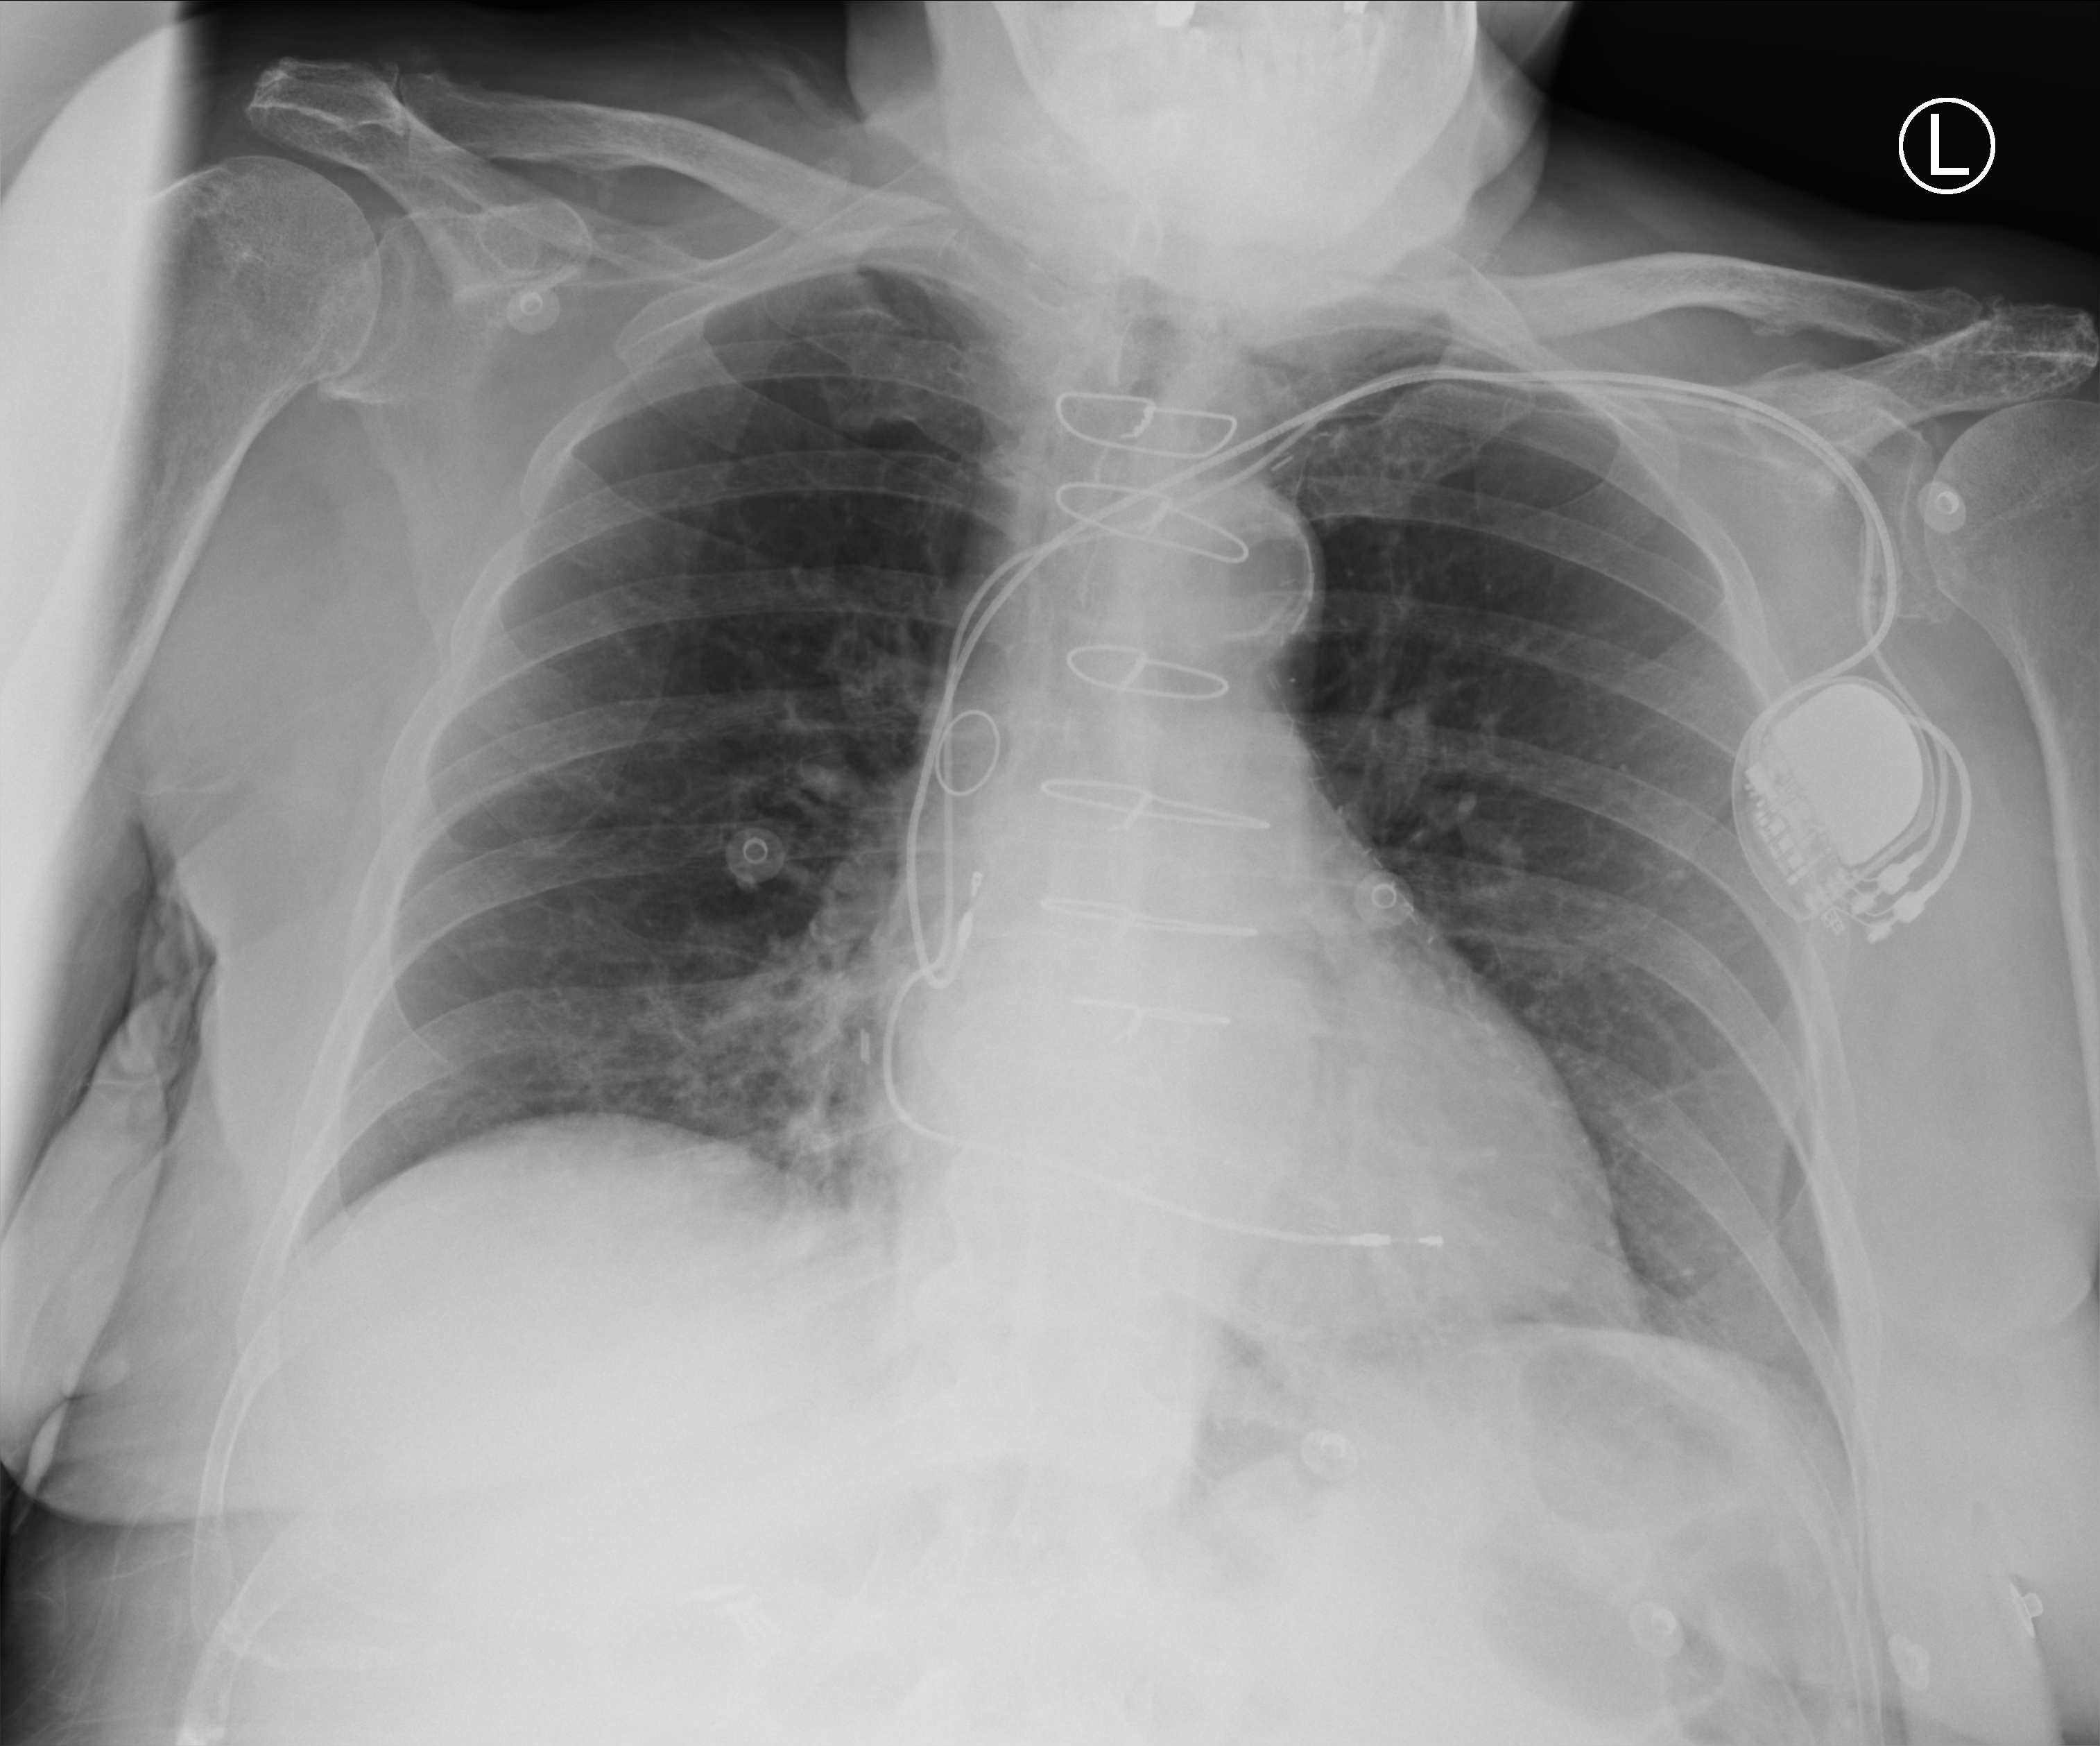
Bedside chest radiograph (computed radiography); anteroposterior (AP) projection. Female patient hospitalised with COVID-19, age 75–90 years.
From the hospital-stay record, not from the radiograph (when in the stay this image was taken is not recorded):
- admitted to intensive care during this hospital stay: no